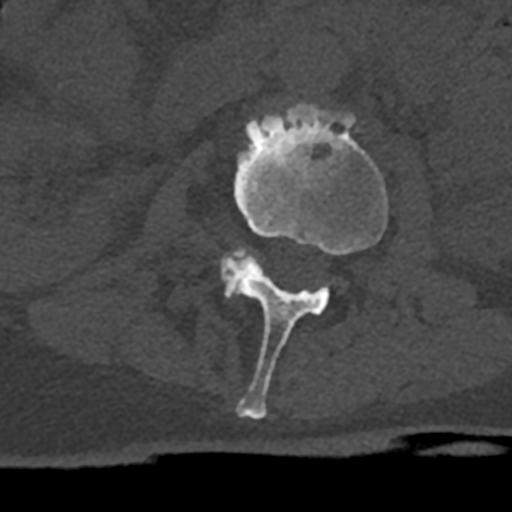
CT including the spine, one axial slice; slice 366 of 797 in the series (ordered by position); reconstruction kernel Br40s/3; 120 kVp; bone window (W 1800 / L 400 HU); 0.5 mm slice thickness; 512 × 512 image matrix, field of view 160 × 160 mm. Male patient, age 74 years. Case-level facts recorded for this patient, not image findings: primary cancer: renal; vertebrae with lytic lesions (as recorded): T10, L1, L2, L3, L4, L5.
Annotated regions visible in this slice (semi-automatically segmented with operator editing):
- L2 vertebra: box from (x=220, y=104) to (x=388, y=420) px
- L3 vertebra: (x=222, y=248)–(x=259, y=298)